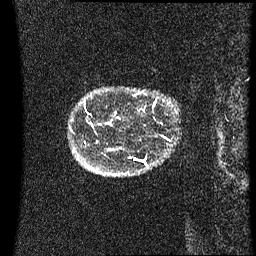
Breast MRI (dynamic contrast-enhanced), one sagittal slice; position 1 of 60 along the scan axis; dynamic contrast-enhanced series, image 2 of 3 at this slice position (ordered by acquisition); 1.5 T; TE 4.2 ms, TR 8.4 ms; 2.2 mm slice thickness; 256 × 256 image matrix. Patient: female, 41 years. Case-level facts recorded for this patient, not image findings: setting: breast cancer imaged before/during neoadjuvant chemotherapy; receptor status: HER2-positive.
Annotated regions visible in this slice (semi-automatically segmented with operator editing):
- analysis volume of interest (the breast-tissue region the enhancement analysis was run in; not a lesion): bounding box <140,94,157,105> (left, top, right, bottom; pixels)
- tumour enhancement mask (voxels above the 70 % enhancement threshold inside the analysis volume of interest): <155,102,157,105>